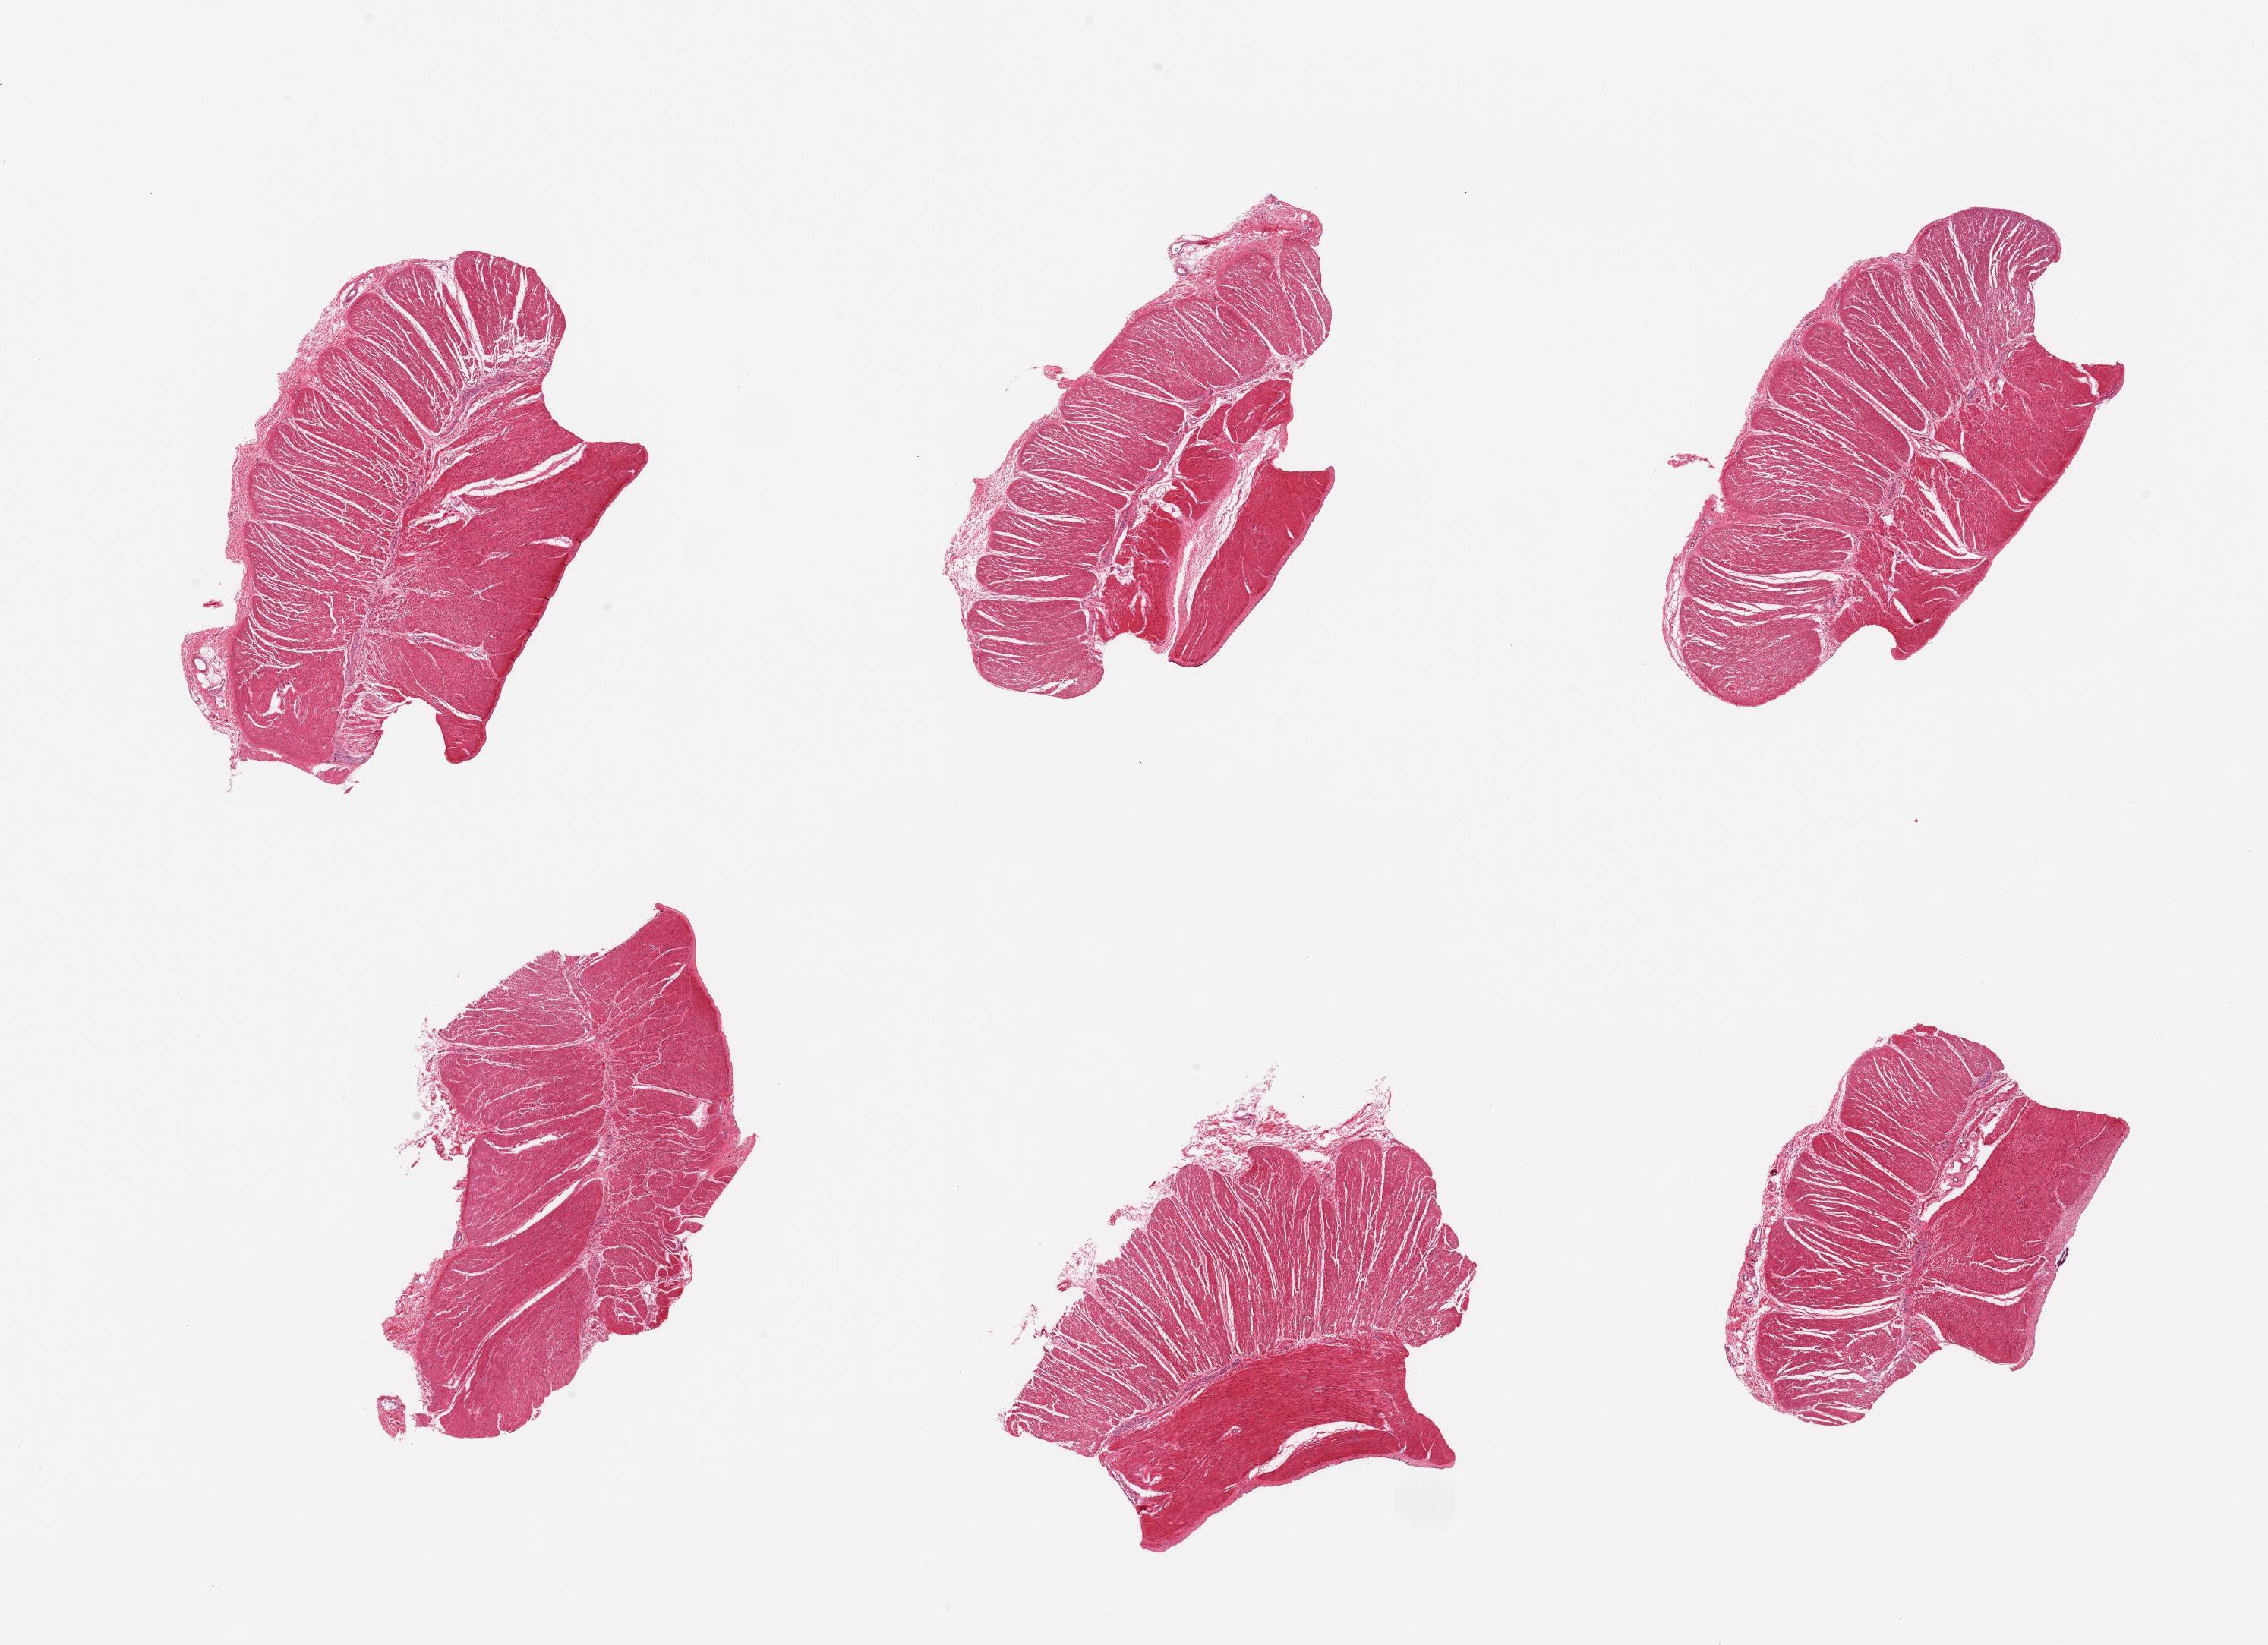
Digitized H&E-stained section — a low-resolution overview of the entire scanned area, about 23.6 x 17.1 mm, PAXgene-fixed paraffin-embedded (PFPE) section, section of sigmoid colon (target tissue), tissue donor sample. Female donor.
- pathologist's review note for this sample: 6 pieces, confirmed target muscularis